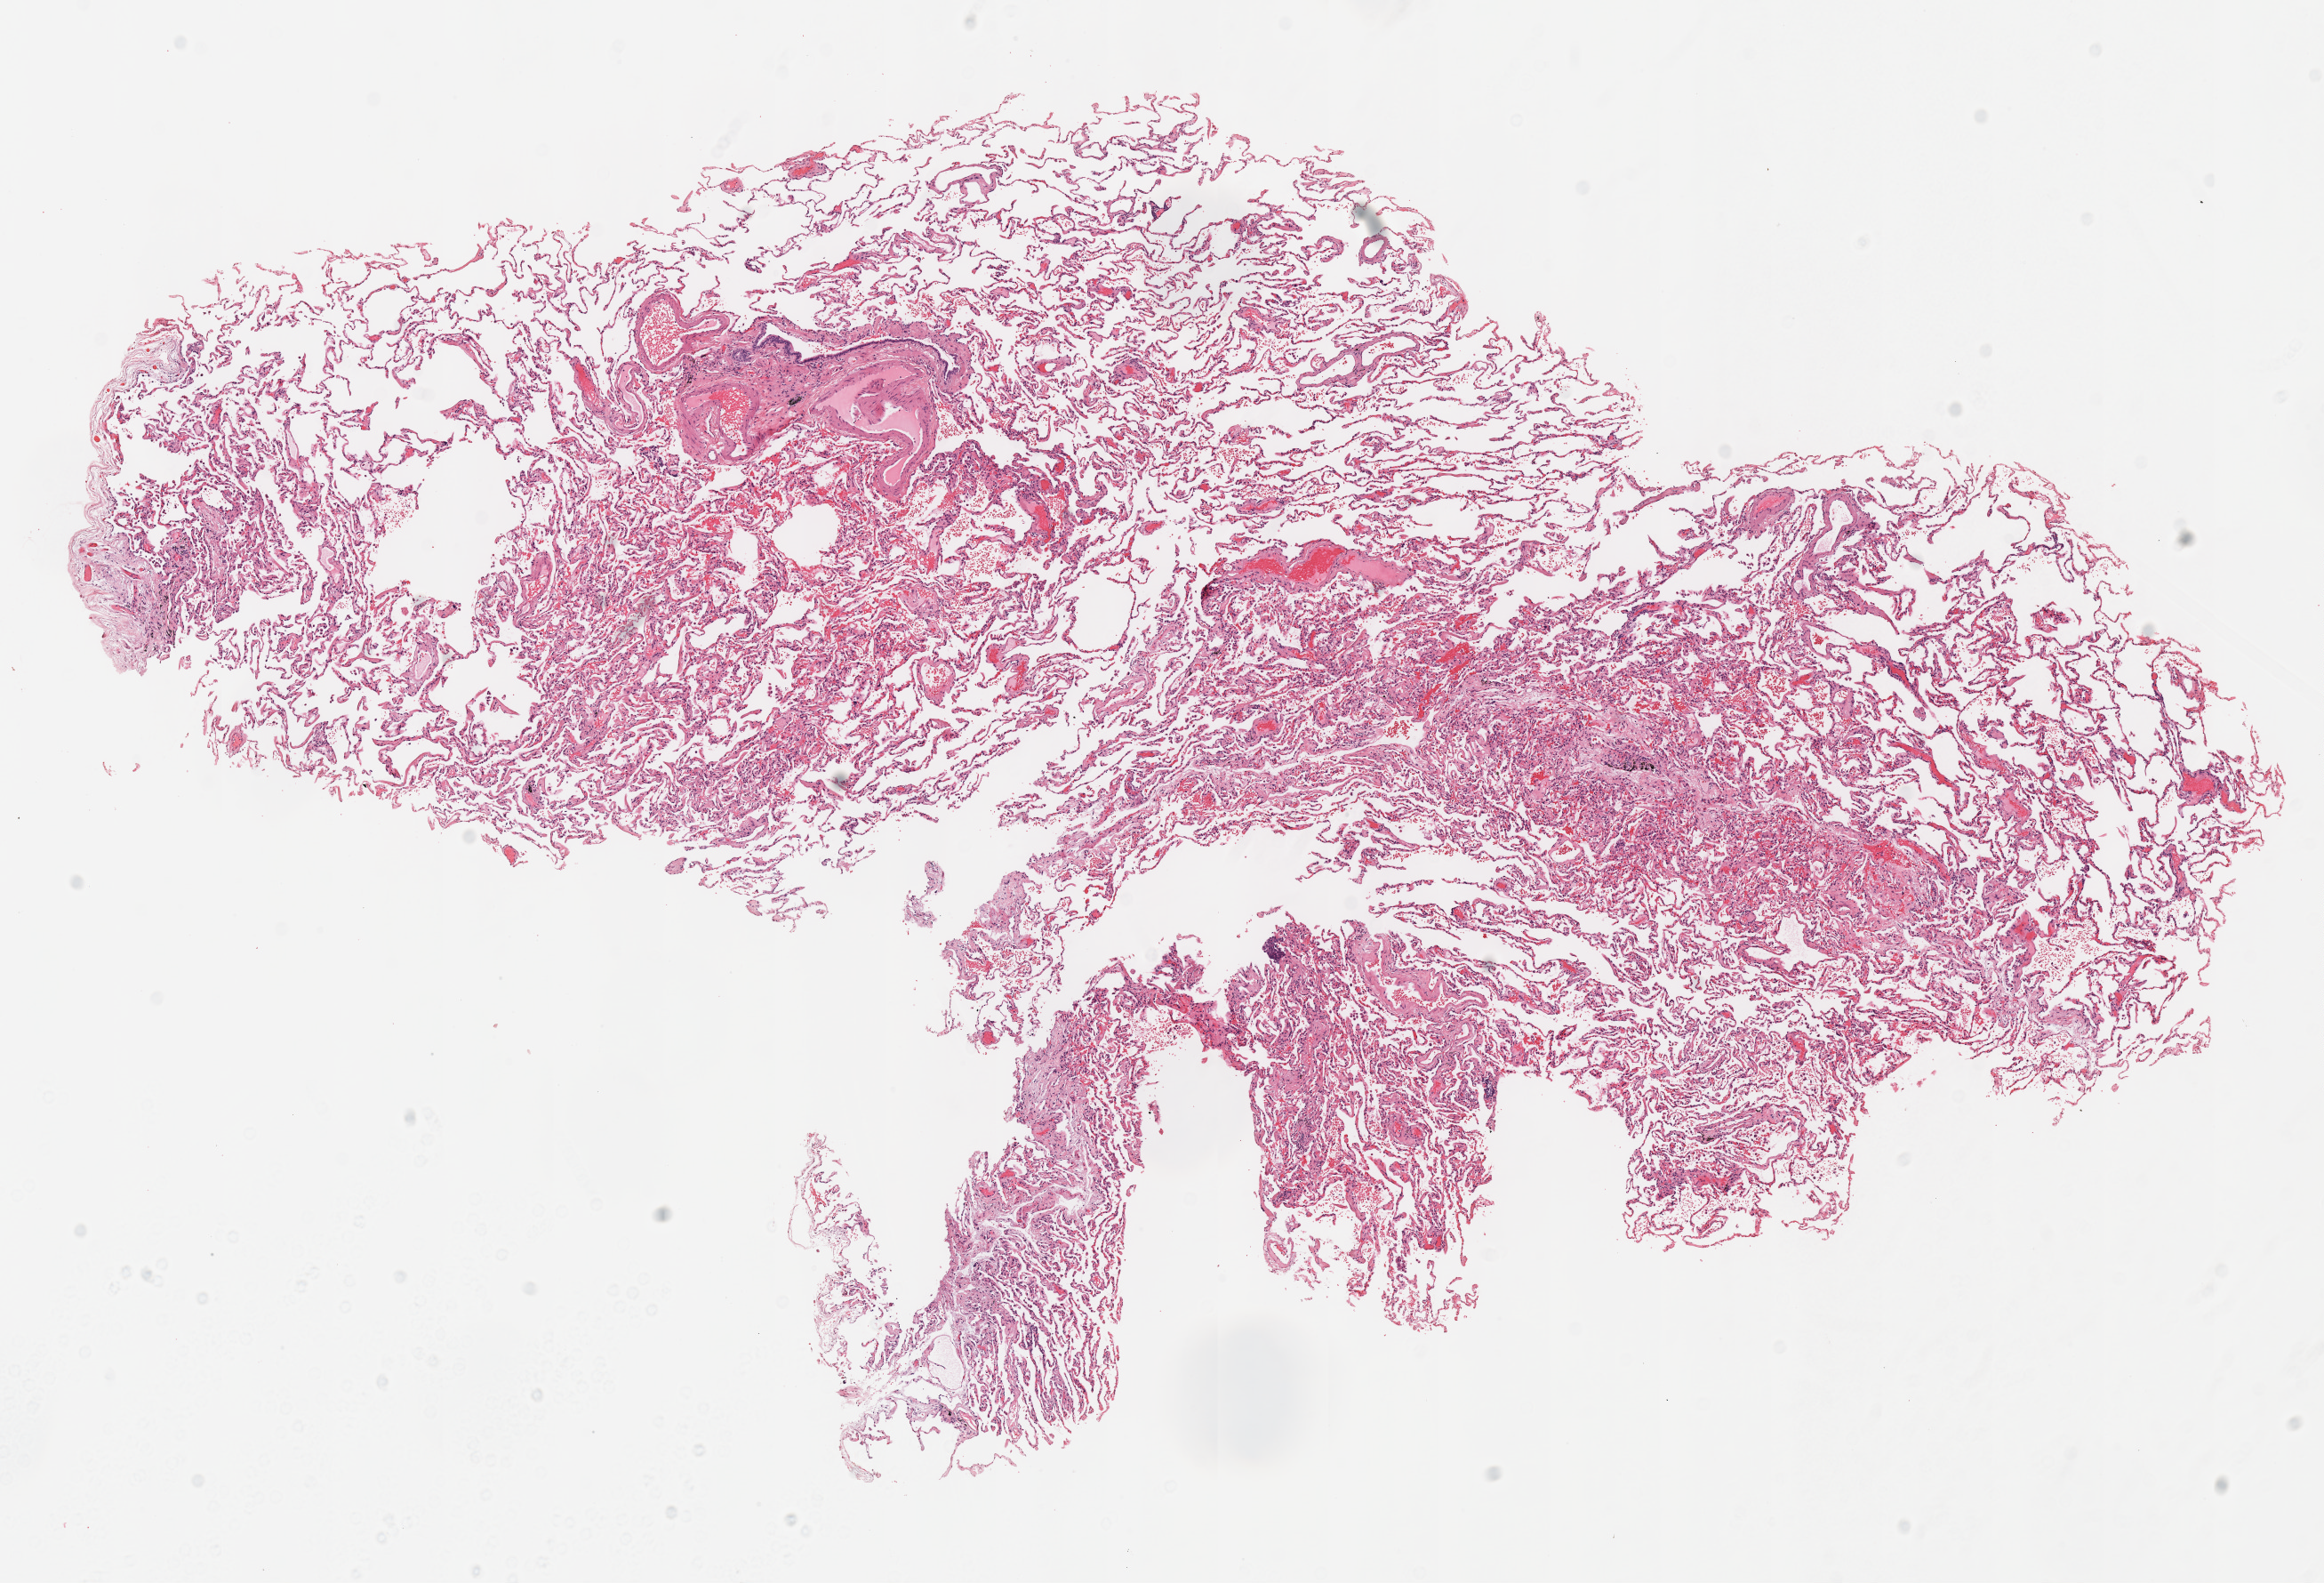
H&E whole-slide image, a low-resolution overview of the entire scanned area, about 10.3 x 7.0 mm (from a 40x scan), frozen section from the top of the tissue portion, lung, solid tissue normal (non-tumour tissue) sample. Patient: female, age at initial diagnosis 75 years.
This section: solid tissue normal sample (biorepository sample class). Patient diagnosis: Squamous cell carcinoma, NOS (upper lobe, lung).